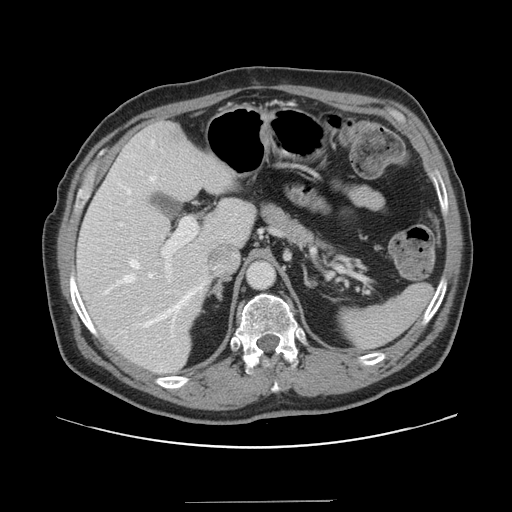
Contrast-enhanced abdominal CT, one axial slice; position 98 of 151 along the scan axis; 120 kVp; intravenous contrast given; soft-tissue window (W 400 / L 40 HU); 512 × 512 image matrix. Male patient, age 63 years. Case-level facts recorded for this patient, not image findings: diagnosis: colorectal cancer liver metastases, imaged before liver resection; multiple liver metastases: no; largest metastasis: 2.1 cm; disease in both lobes: no.
Annotated regions visible in this slice (expert manual segmentation):
- hepatic veins: bounding box <106,176,206,337> (left, top, right, bottom; pixels)
- liver: <78,123,255,372>
- planned liver remnant (the part of the liver to remain after resection): <78,123,253,373>
- portal vein (with intrahepatic branches): <143,217,197,313>